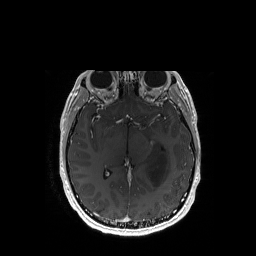
Brain MRI from a brain-tumour surgery series, one axial slice; slice 96 of 192 in the series (ordered by position); T1-weighted post-contrast; 1 mm slice thickness; 256 × 256 image matrix. From the clinical record (not read from this slice): histopathology: Astrocytoma; WHO grade: 3; IDH mutation: yes; tumour location: Left Temporal.
Structures marked on this image (manually delineated by an expert):
- tumour: box from (x=147, y=146) to (x=169, y=187) px